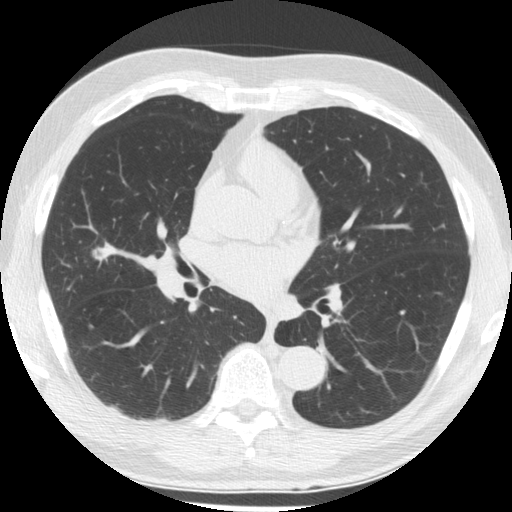
Axial slice from a low-dose chest CT screening exam. First (baseline) screen. Lung window (W 1500 / L -600 HU). 2.5 mm slice thickness. Standard (soft-tissue) reconstruction kernel (STANDARD). 120 kVp. Male participant, aged 64 years at enrolment. Former smoker at enrolment.
• Expert reader's lesion annotation, bounding box (x1, y1, x2, y2) in pixels: (57, 221, 128, 286).
• The screening reader recorded 2 non-calcified nodules or masses ≥4 mm on this exam; which of them this box marks is not recorded.
• Official screen result: positive, change unspecified: nodule(s) >= 4 mm or enlarging nodule(s), mass(es), or other non-specific abnormalities suspicious for lung cancer.